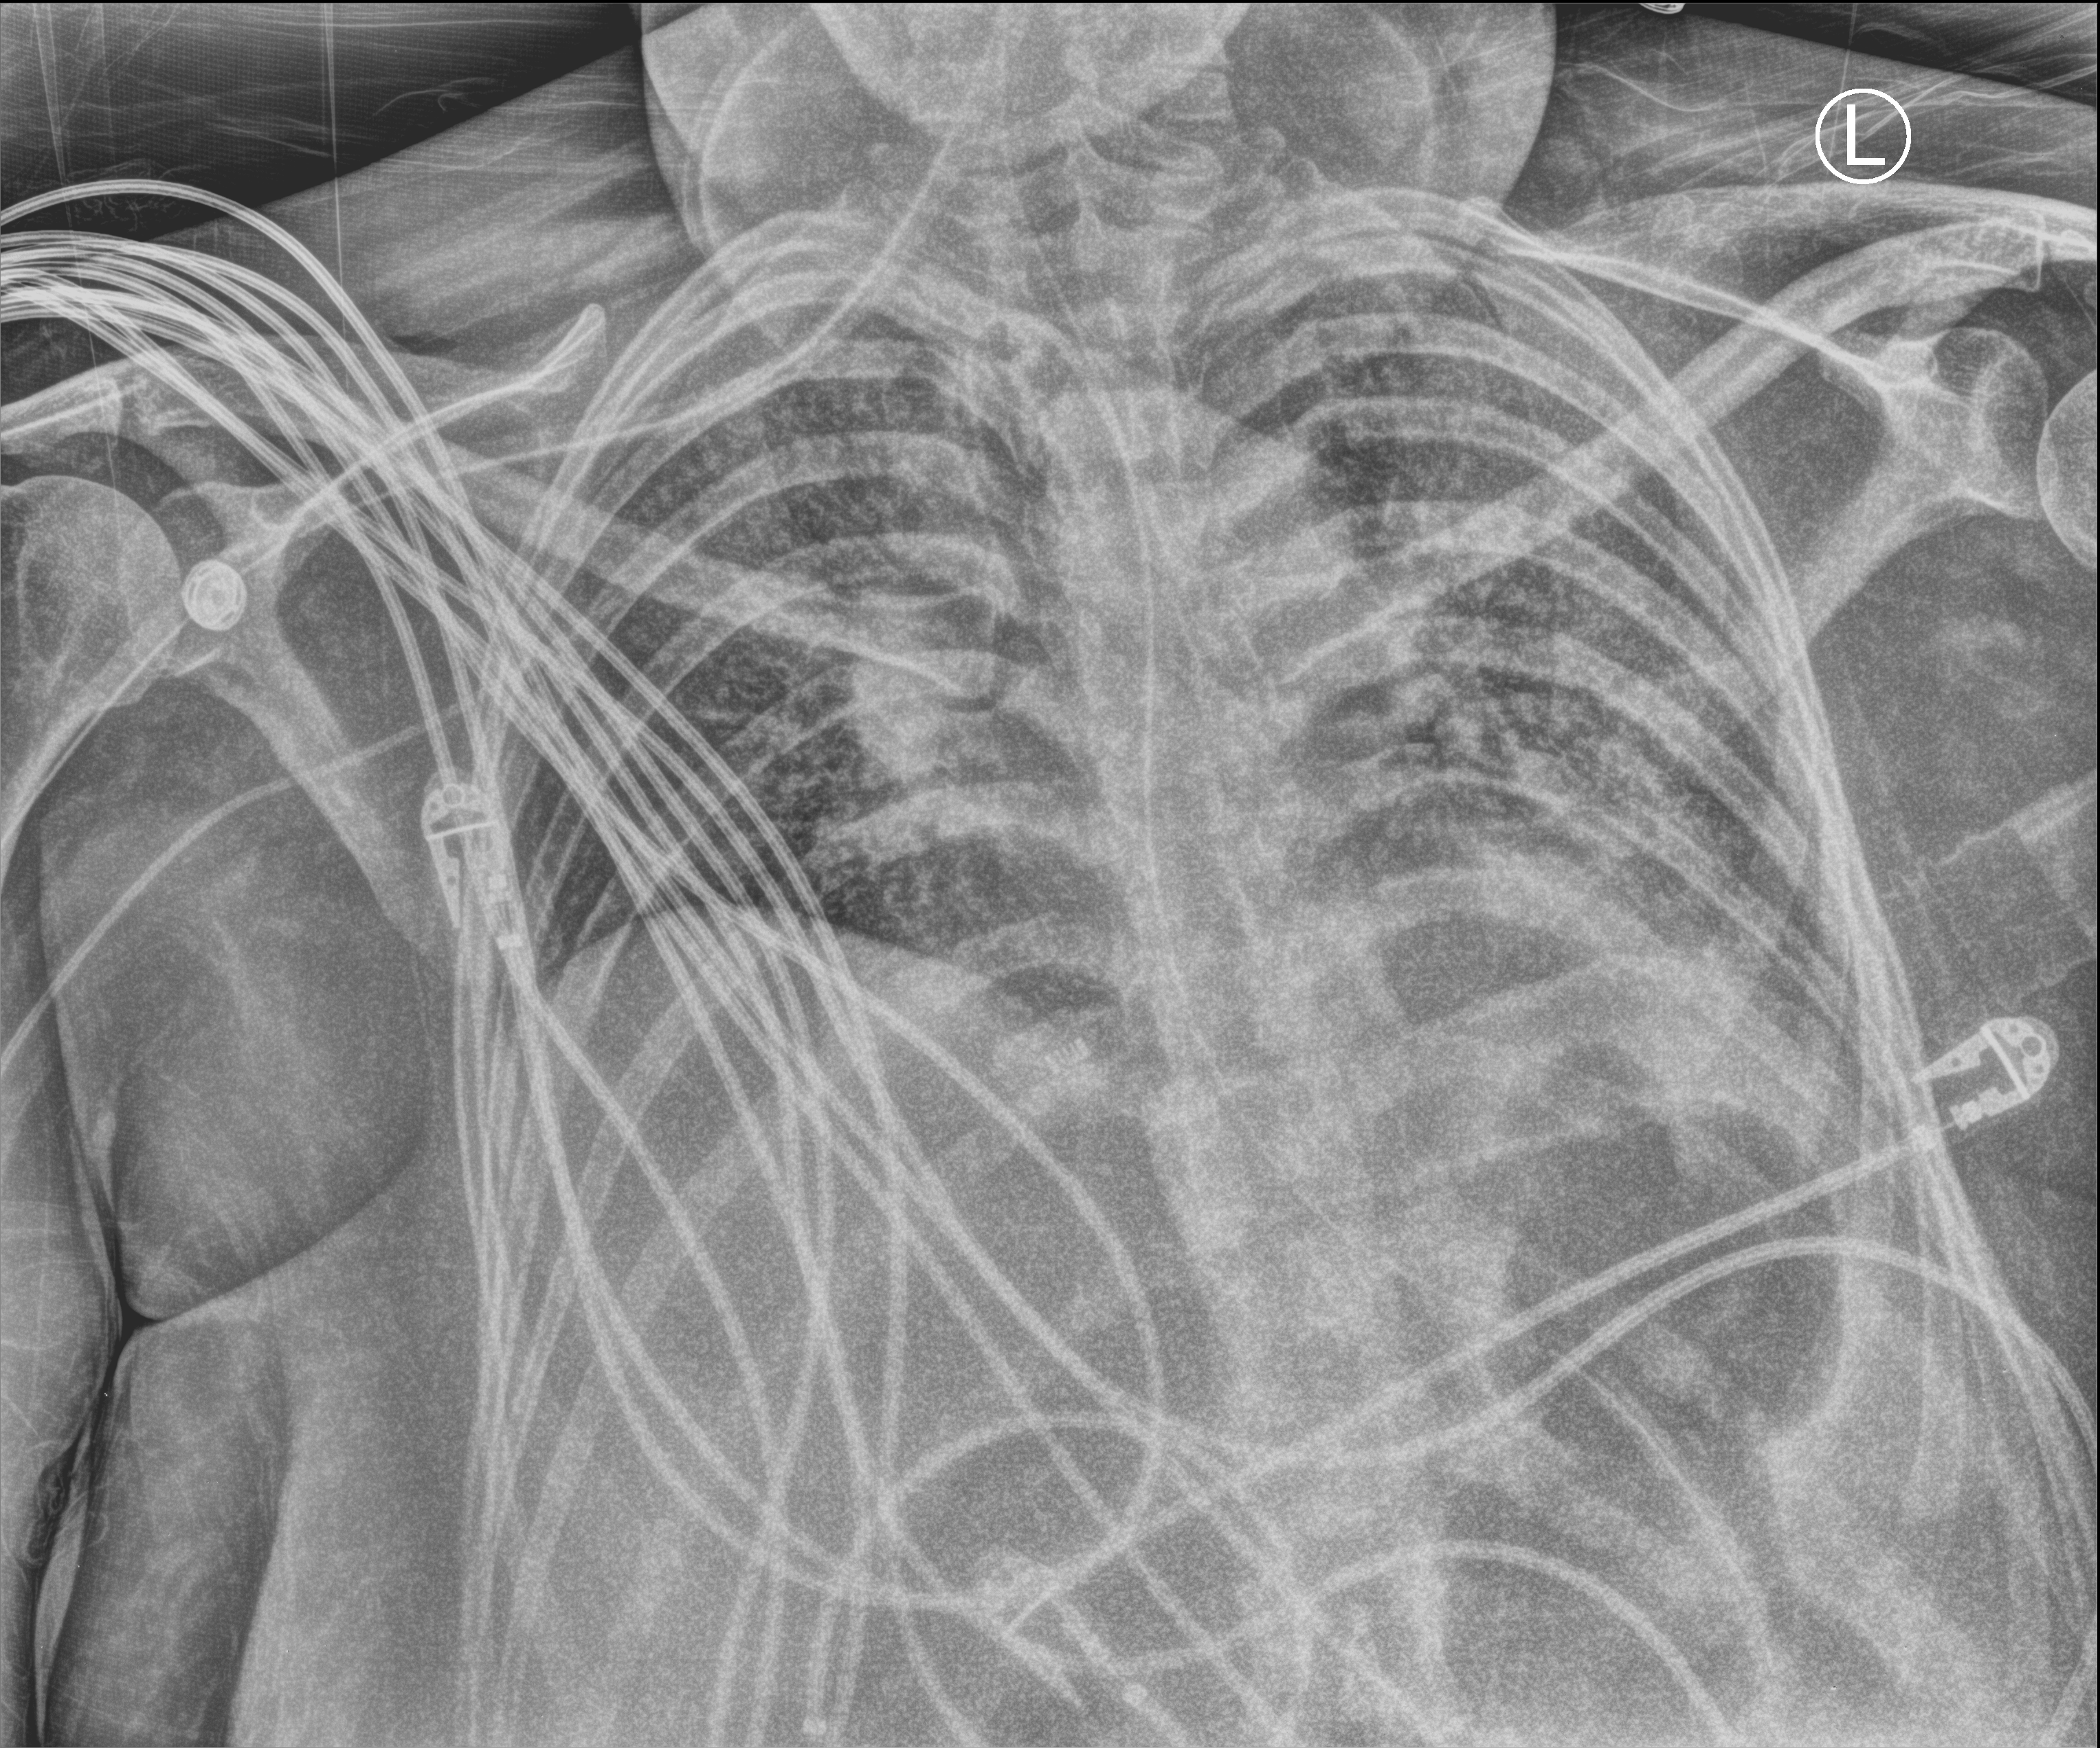
Bedside chest radiograph (computed radiography); anteroposterior (AP) projection. Female patient hospitalised with COVID-19, age 18–59 years.
Hospital-stay facts (about this admission, not read from this image; timing relative to this image not recorded): smoking status (admission record): former; admitted to intensive care during this hospital stay: yes; mechanically ventilated during this hospital stay: yes.